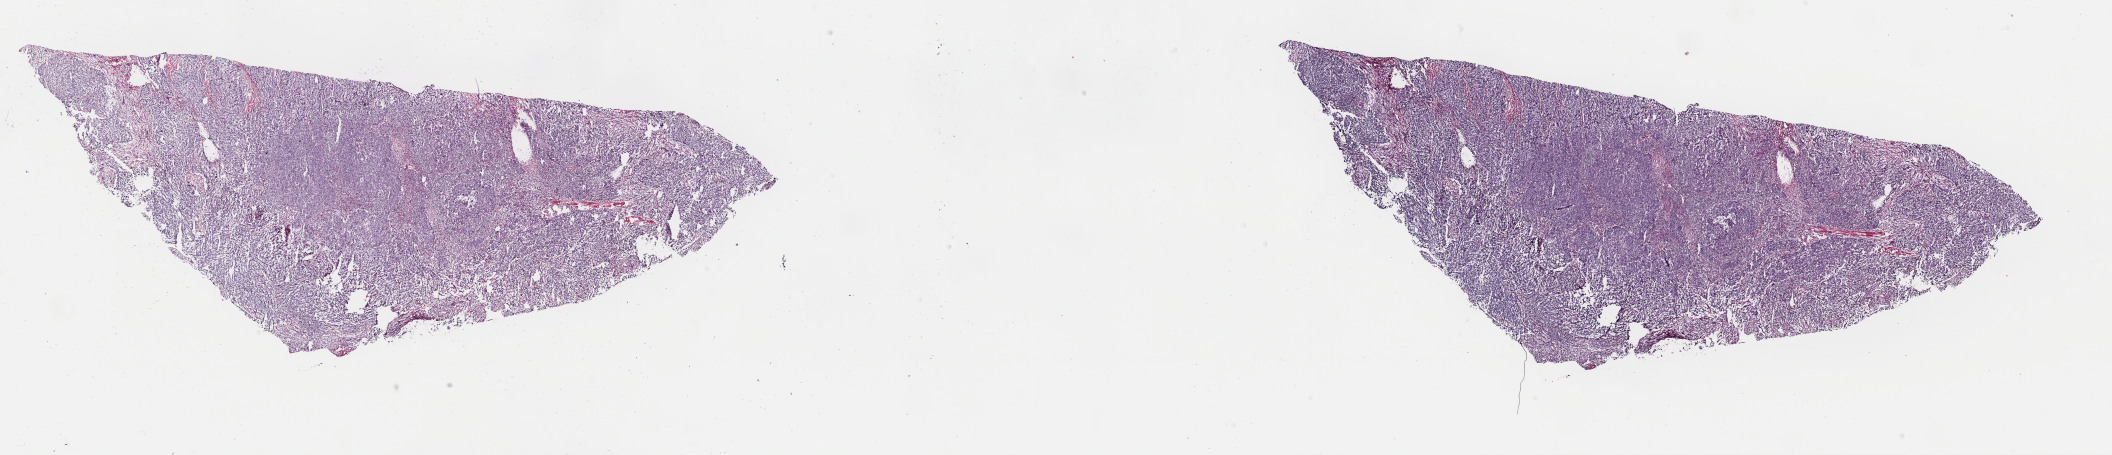
H&E whole-slide image, whole scanned area (about 33.4 x 7.2 mm) shown as a low-resolution overview. Frozen section from the top of the tissue portion. Sample: primary tumour, bladder. Male, age 74 years at initial diagnosis. Histologic grade: high grade. Composition of this section per pathologist review: tumour cells 80%, tumour nuclei 90%, normal cells 0%, stromal cells 20%, necrosis 0%. Inflammatory infiltration, as recorded: lymphocyte infiltration 0%, monocyte infiltration 0%, neutrophil infiltration 0%.
AJCC pathologic stage: II. Lymph nodes positive (case pathology): 0 of 15 examined. Diagnosis: Transitional cell carcinoma (dome of bladder).